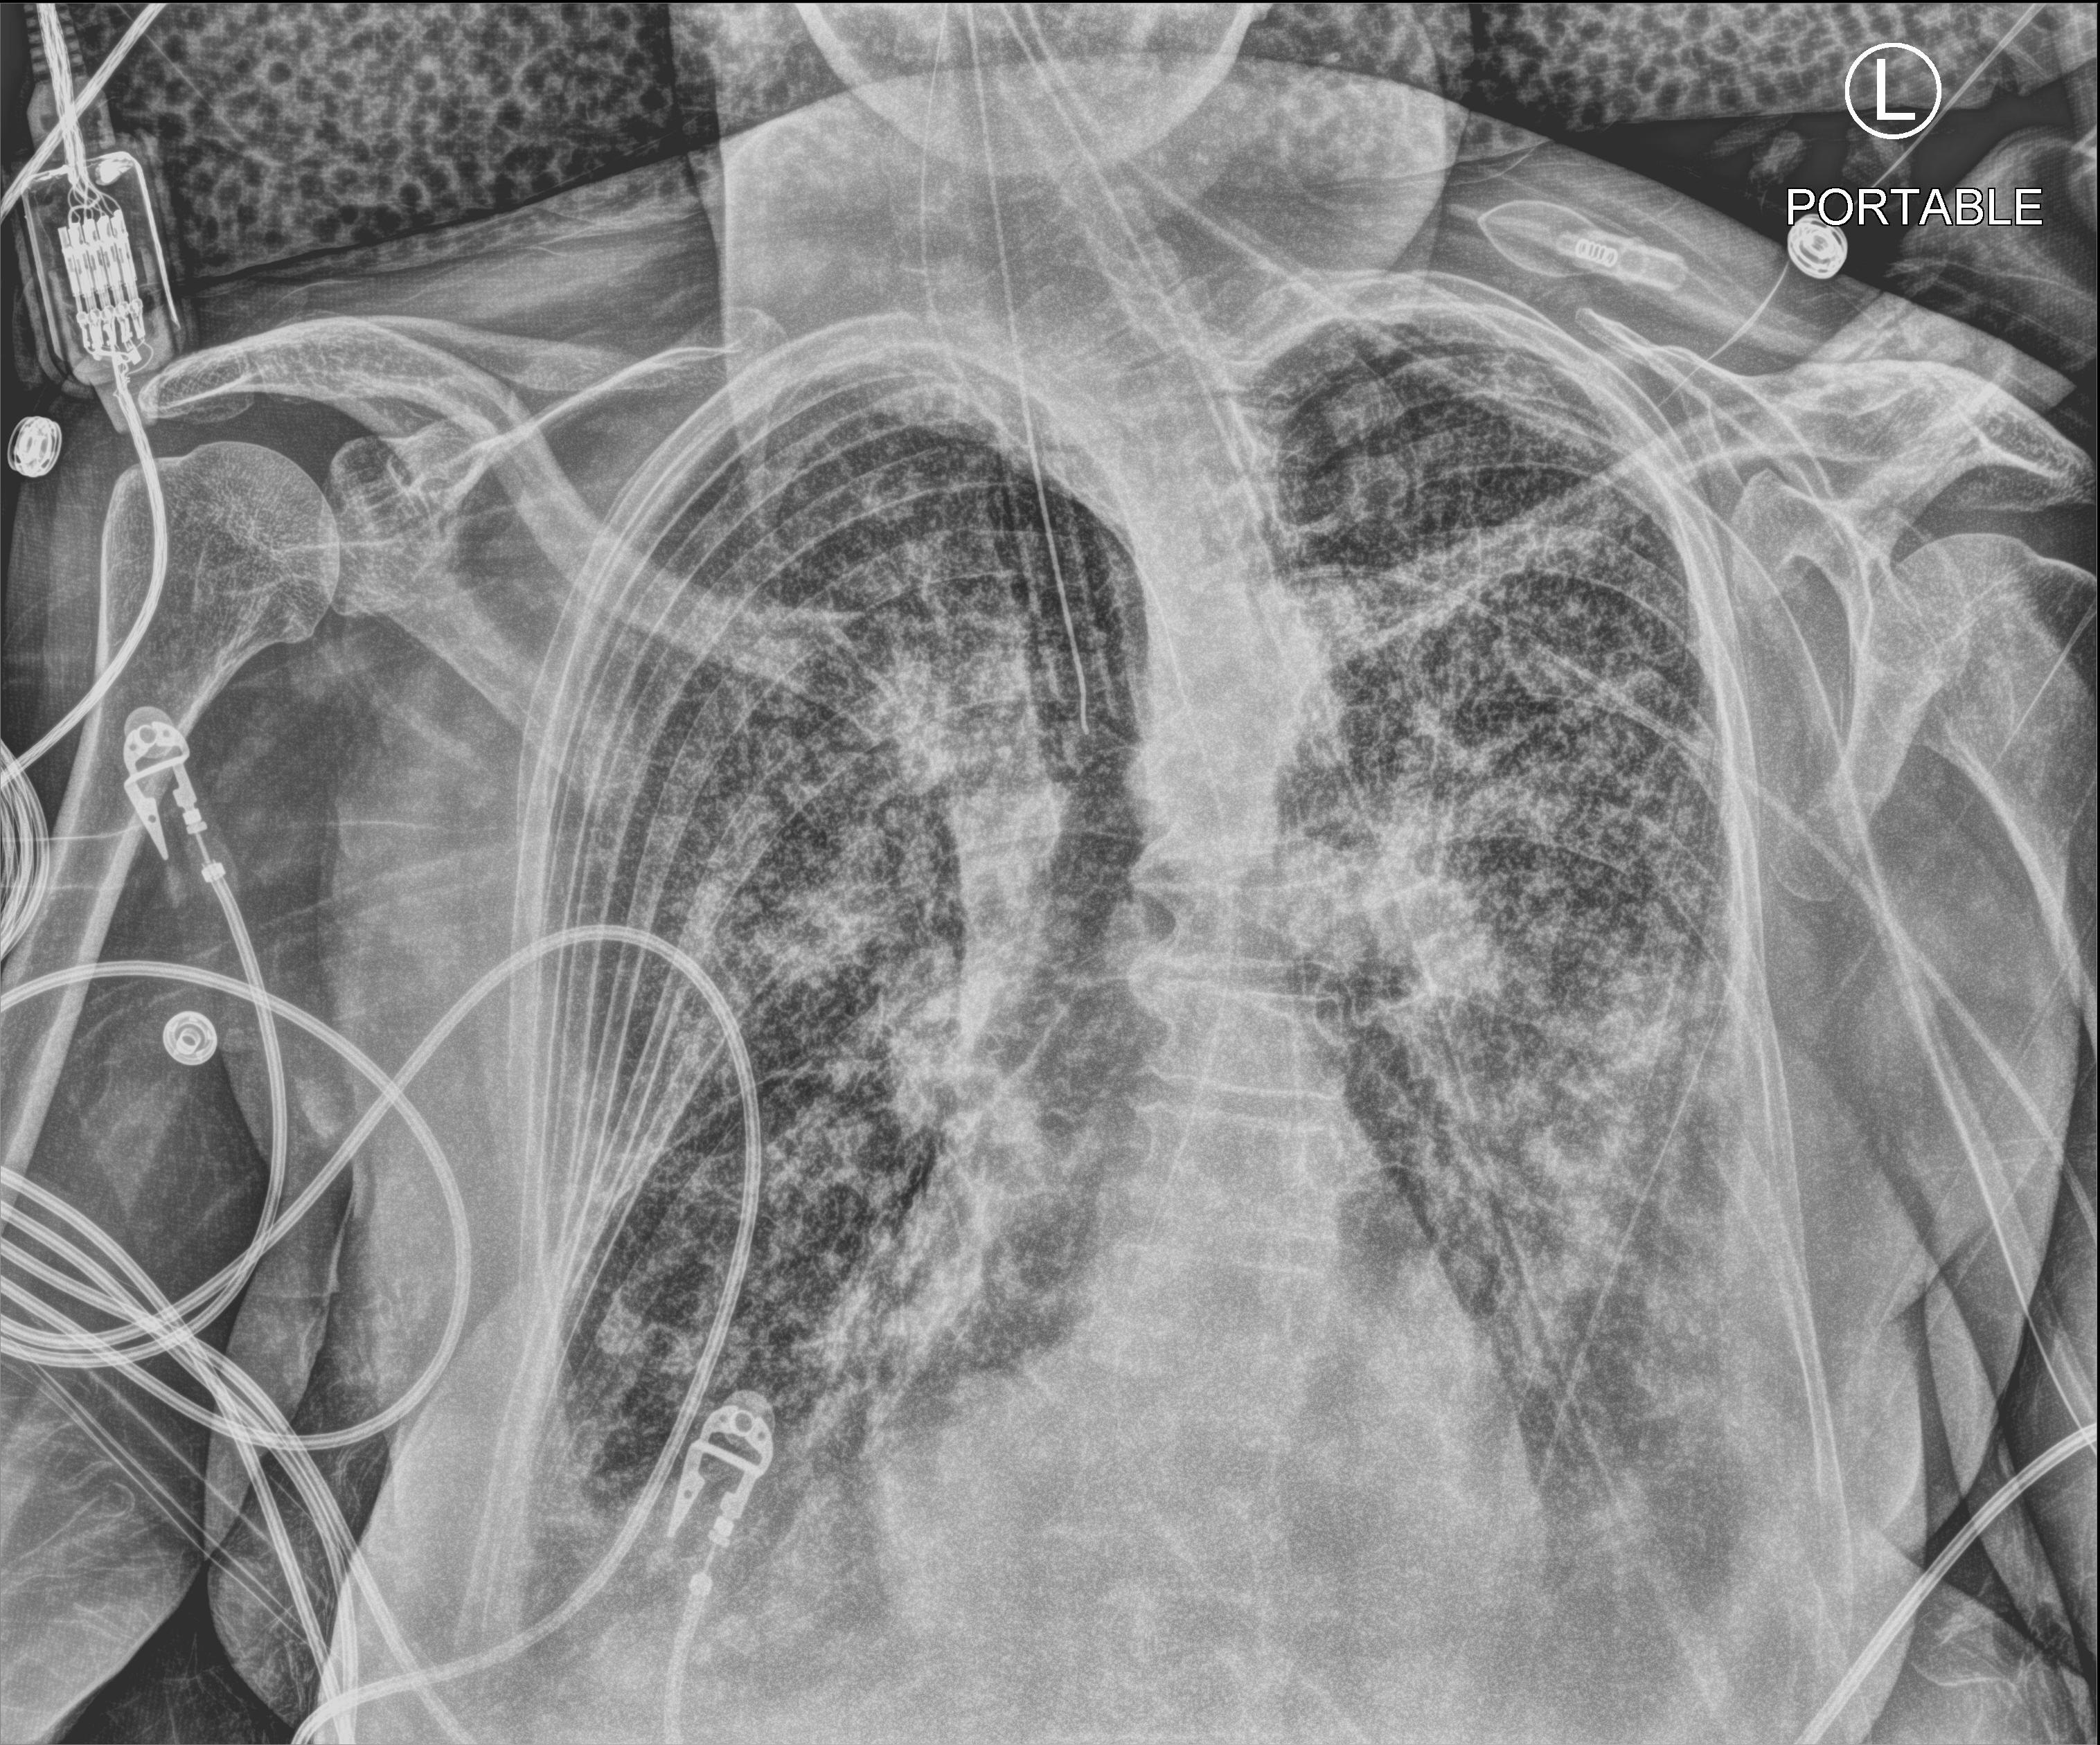
Chest X-ray (portable). Female patient hospitalised with COVID-19, age 75–90 years.
From the hospital-stay record, not from the radiograph (when in the stay this image was taken is not recorded): diabetes (admission record): no; mechanically ventilated during this hospital stay: yes; admitted to intensive care during this hospital stay: yes.